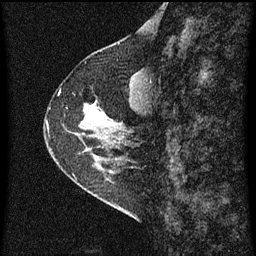
Breast MRI (dynamic contrast-enhanced), one sagittal slice; slice 23 of 60 in the series (ordered by position); dynamic contrast-enhanced series, image 2 of 3 at this slice position (ordered by acquisition); 1.5 T; TE 4.2 ms, TR 8 ms; 256 × 256 image matrix, field of view 180 × 180 mm. Patient: female, 56 years.
Annotated regions visible in this slice (semi-automatically segmented with operator editing):
- analysis volume of interest (the breast-tissue region the enhancement analysis was run in; not a lesion): box from (x=49, y=96) to (x=110, y=159) px
- tumour enhancement mask (voxels above the 70 % enhancement threshold inside the analysis volume of interest): (x=85, y=106)–(x=107, y=121)